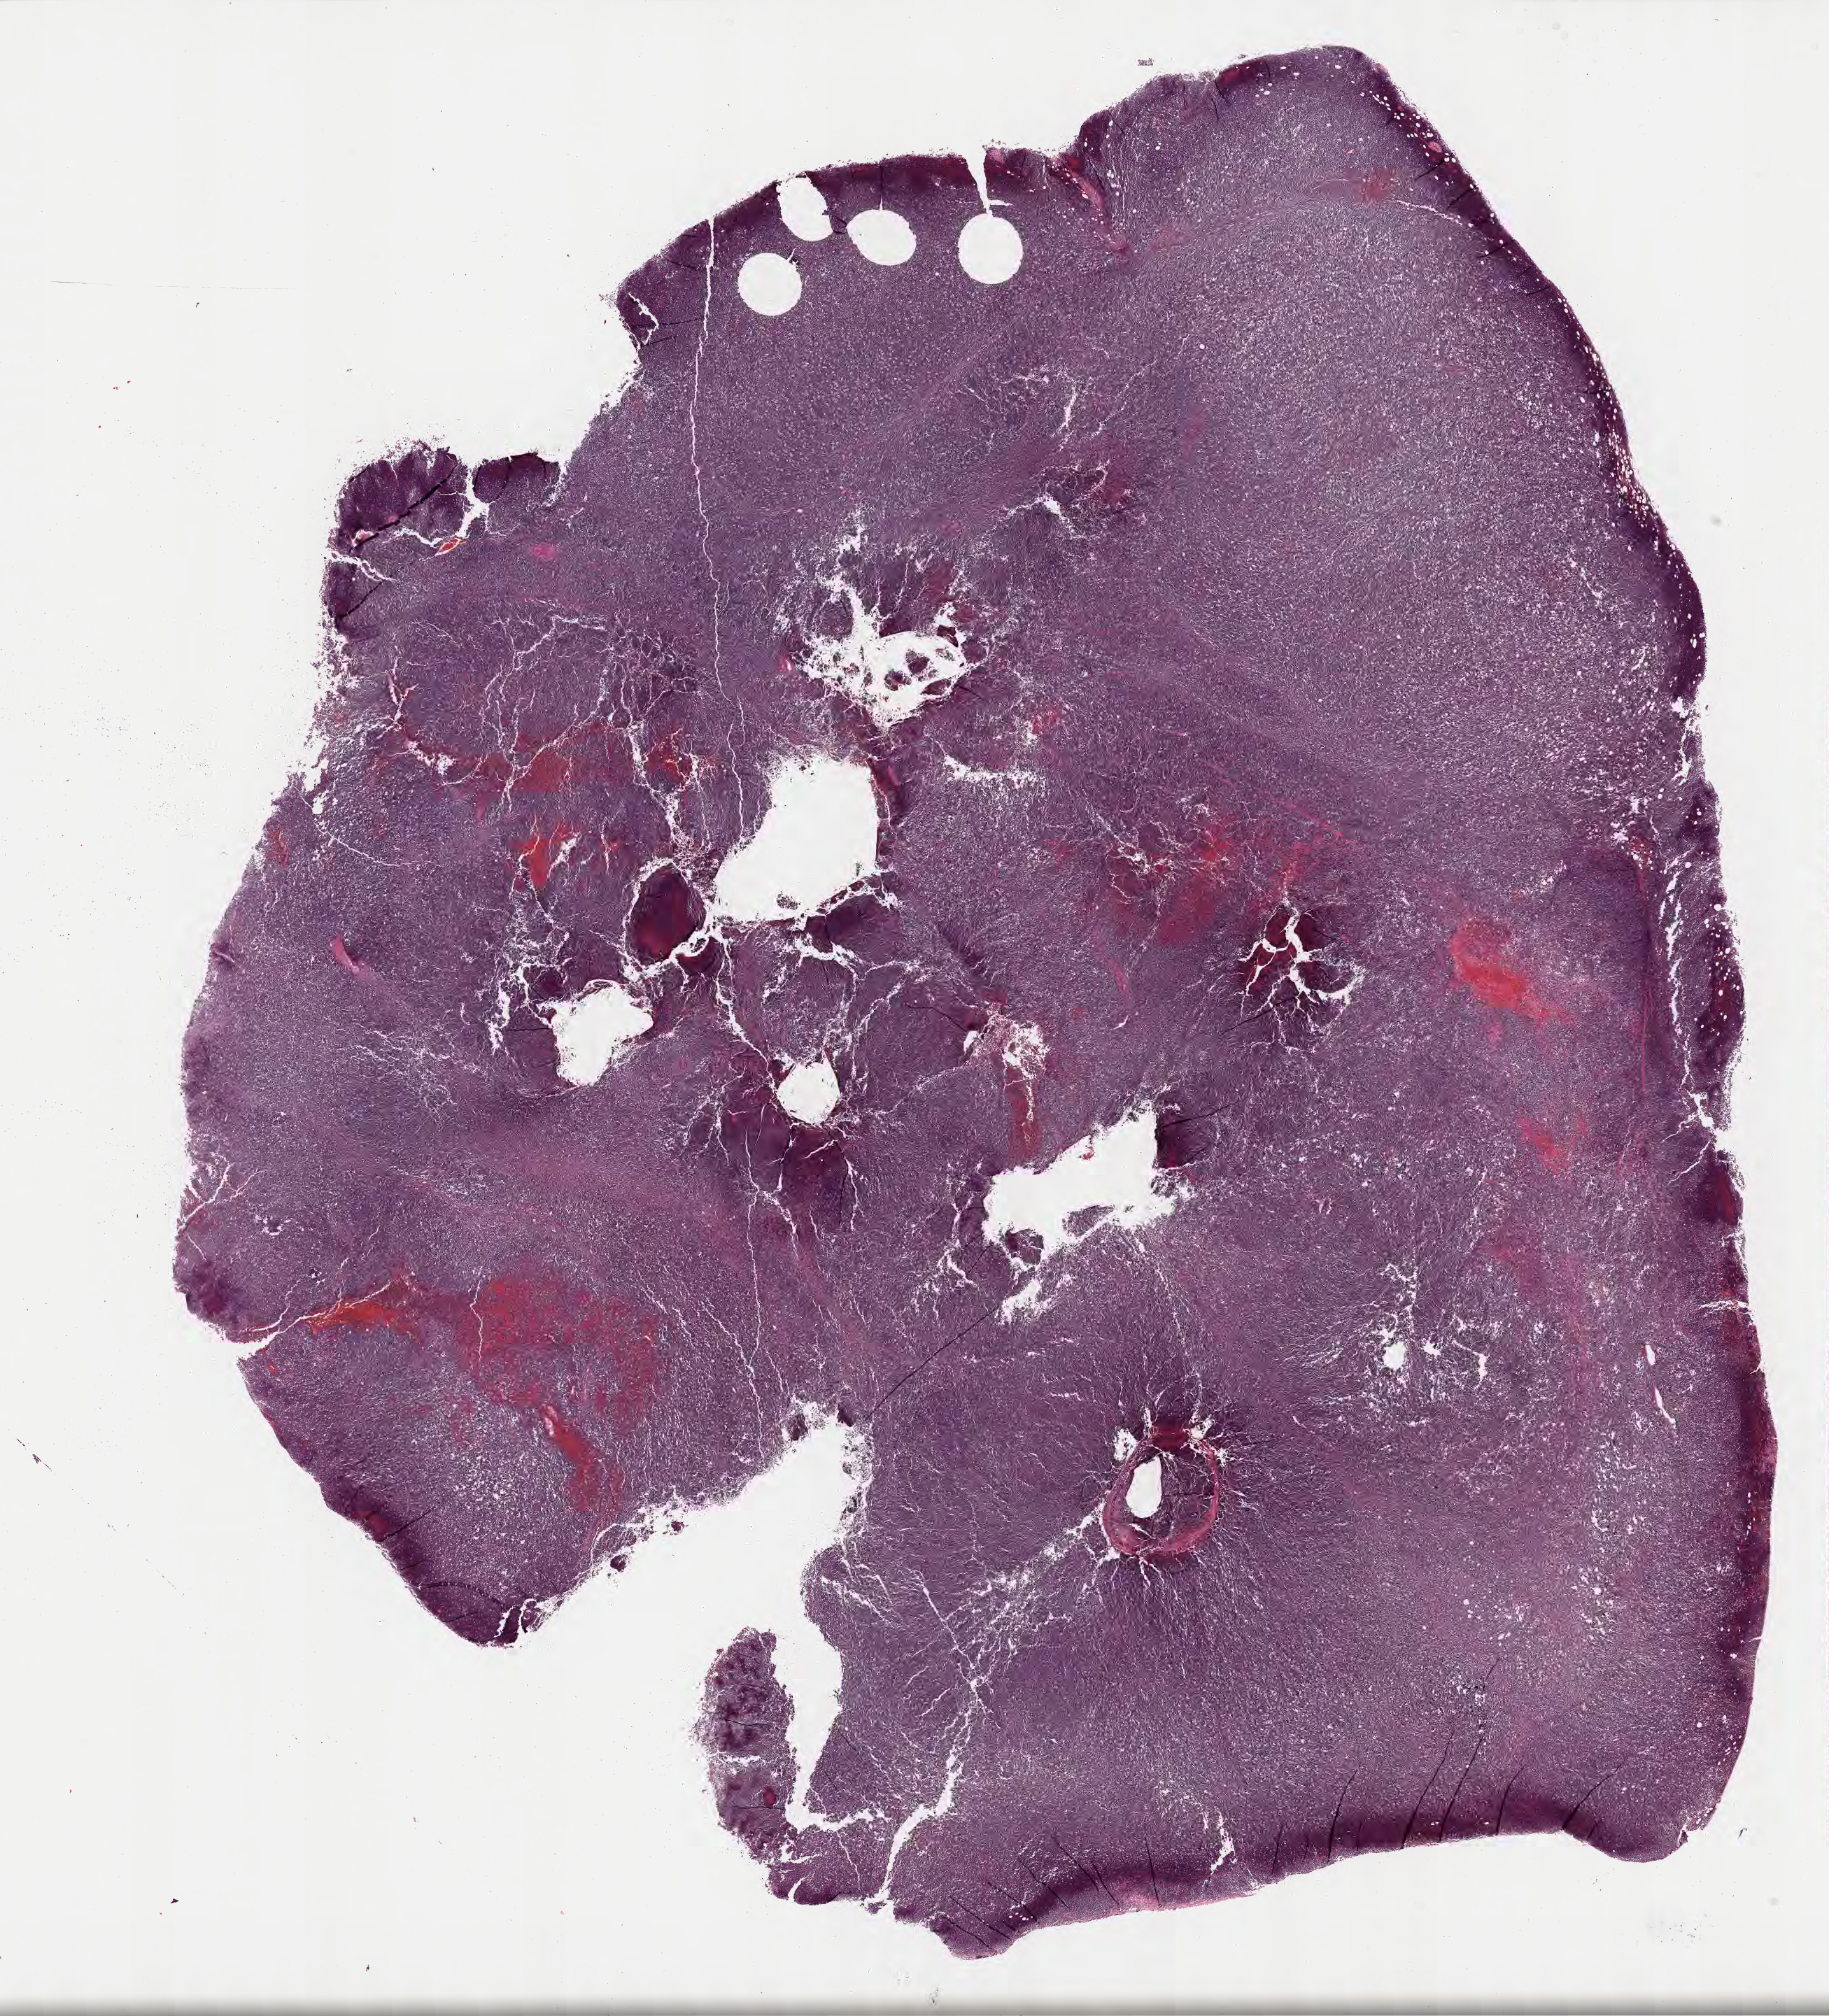
Whole-slide image, haematoxylin and eosin stain, whole scanned area (about 21.1 x 23.3 mm) shown as a low-resolution overview. FFPE section. Specimen: primary tumor. Male patient. Composition of this section per pathologist review: tumor cells 95%, tumor nuclei 90%, stromal cells 5%, necrosis 0%, normal cells 0%. Inflammatory infiltration, as recorded: lymphocyte infiltration 50%, monocyte infiltration 30%, neutrophil infiltration 0%.
Section: bottom of the tissue portion. Ann Arbor stage (patient): Stage IV. Diagnosis: Burkitt lymphoma, NOS.